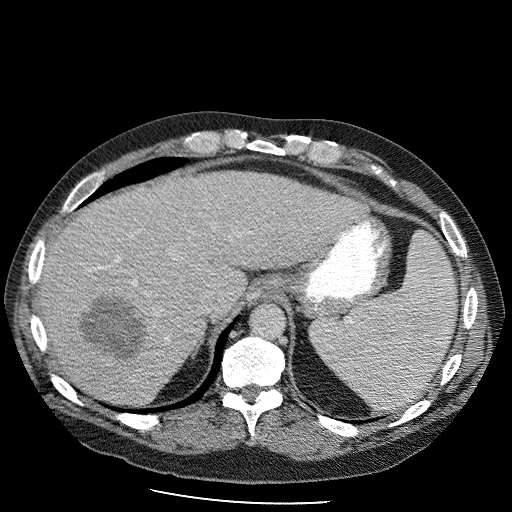
Contrast-enhanced abdominal CT (liver protocol), one axial slice. Slice 78 of 98 in the series (ordered by position). Reconstruction kernel STANDARD. Soft-tissue window (W 400 / L 40 HU). 2.5 mm slice thickness. 512 × 512 image matrix, field of view 400 × 400 mm. Case-level facts recorded for this patient, not image findings: diagnosis: hepatocellular carcinoma (patient treated with transarterial chemoembolisation; whether this scan precedes or follows treatment is not stated here); TNM stage (as recorded): Stage-II; Child-Pugh class: B; tumour differentiation: moderately differentiated; tumour nodularity: uninodular.
Annotated regions visible in this slice (semi-automatic segmentation, software-assisted and operator-edited):
- liver parenchyma outside the tumour (the mass and vessels are separate outlines, so this box may not span the whole liver): box from (x=36, y=170) to (x=366, y=408) px
- mass: (x=75, y=287)–(x=154, y=365)
- liver vessels: (x=106, y=281)–(x=169, y=338)